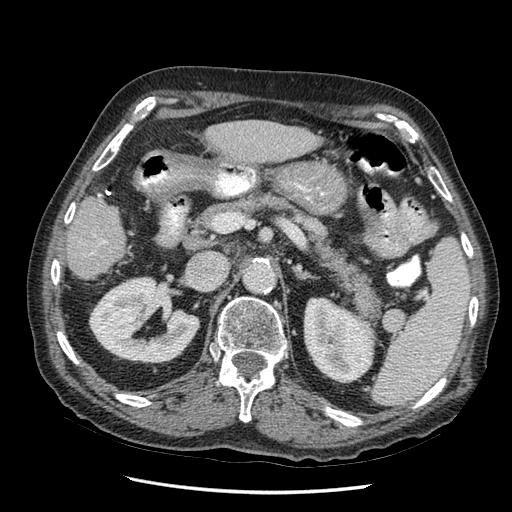
Contrast-enhanced abdominal CT (liver protocol), one axial slice; position 18 of 67 along the scan axis; 120 kVp; soft-tissue window (W 400 / L 40 HU); 2.5 mm slice thickness; 512 × 512 image matrix. From the clinical record (not read from this slice): diagnosis: hepatocellular carcinoma (patient treated with transarterial chemoembolisation; whether this scan precedes or follows treatment is not stated here); TNM stage (as recorded): Stage-I; Child-Pugh class: A; tumour differentiation: moderately differentiated.
Outlined on this slice (semi-automatic segmentation, software-assisted and operator-edited):
- liver parenchyma outside the tumour (the mass and vessels are separate outlines, so this box may not span the whole liver): box from (x=66, y=120) to (x=326, y=282) px
- liver vessels: (x=96, y=140)–(x=253, y=207)